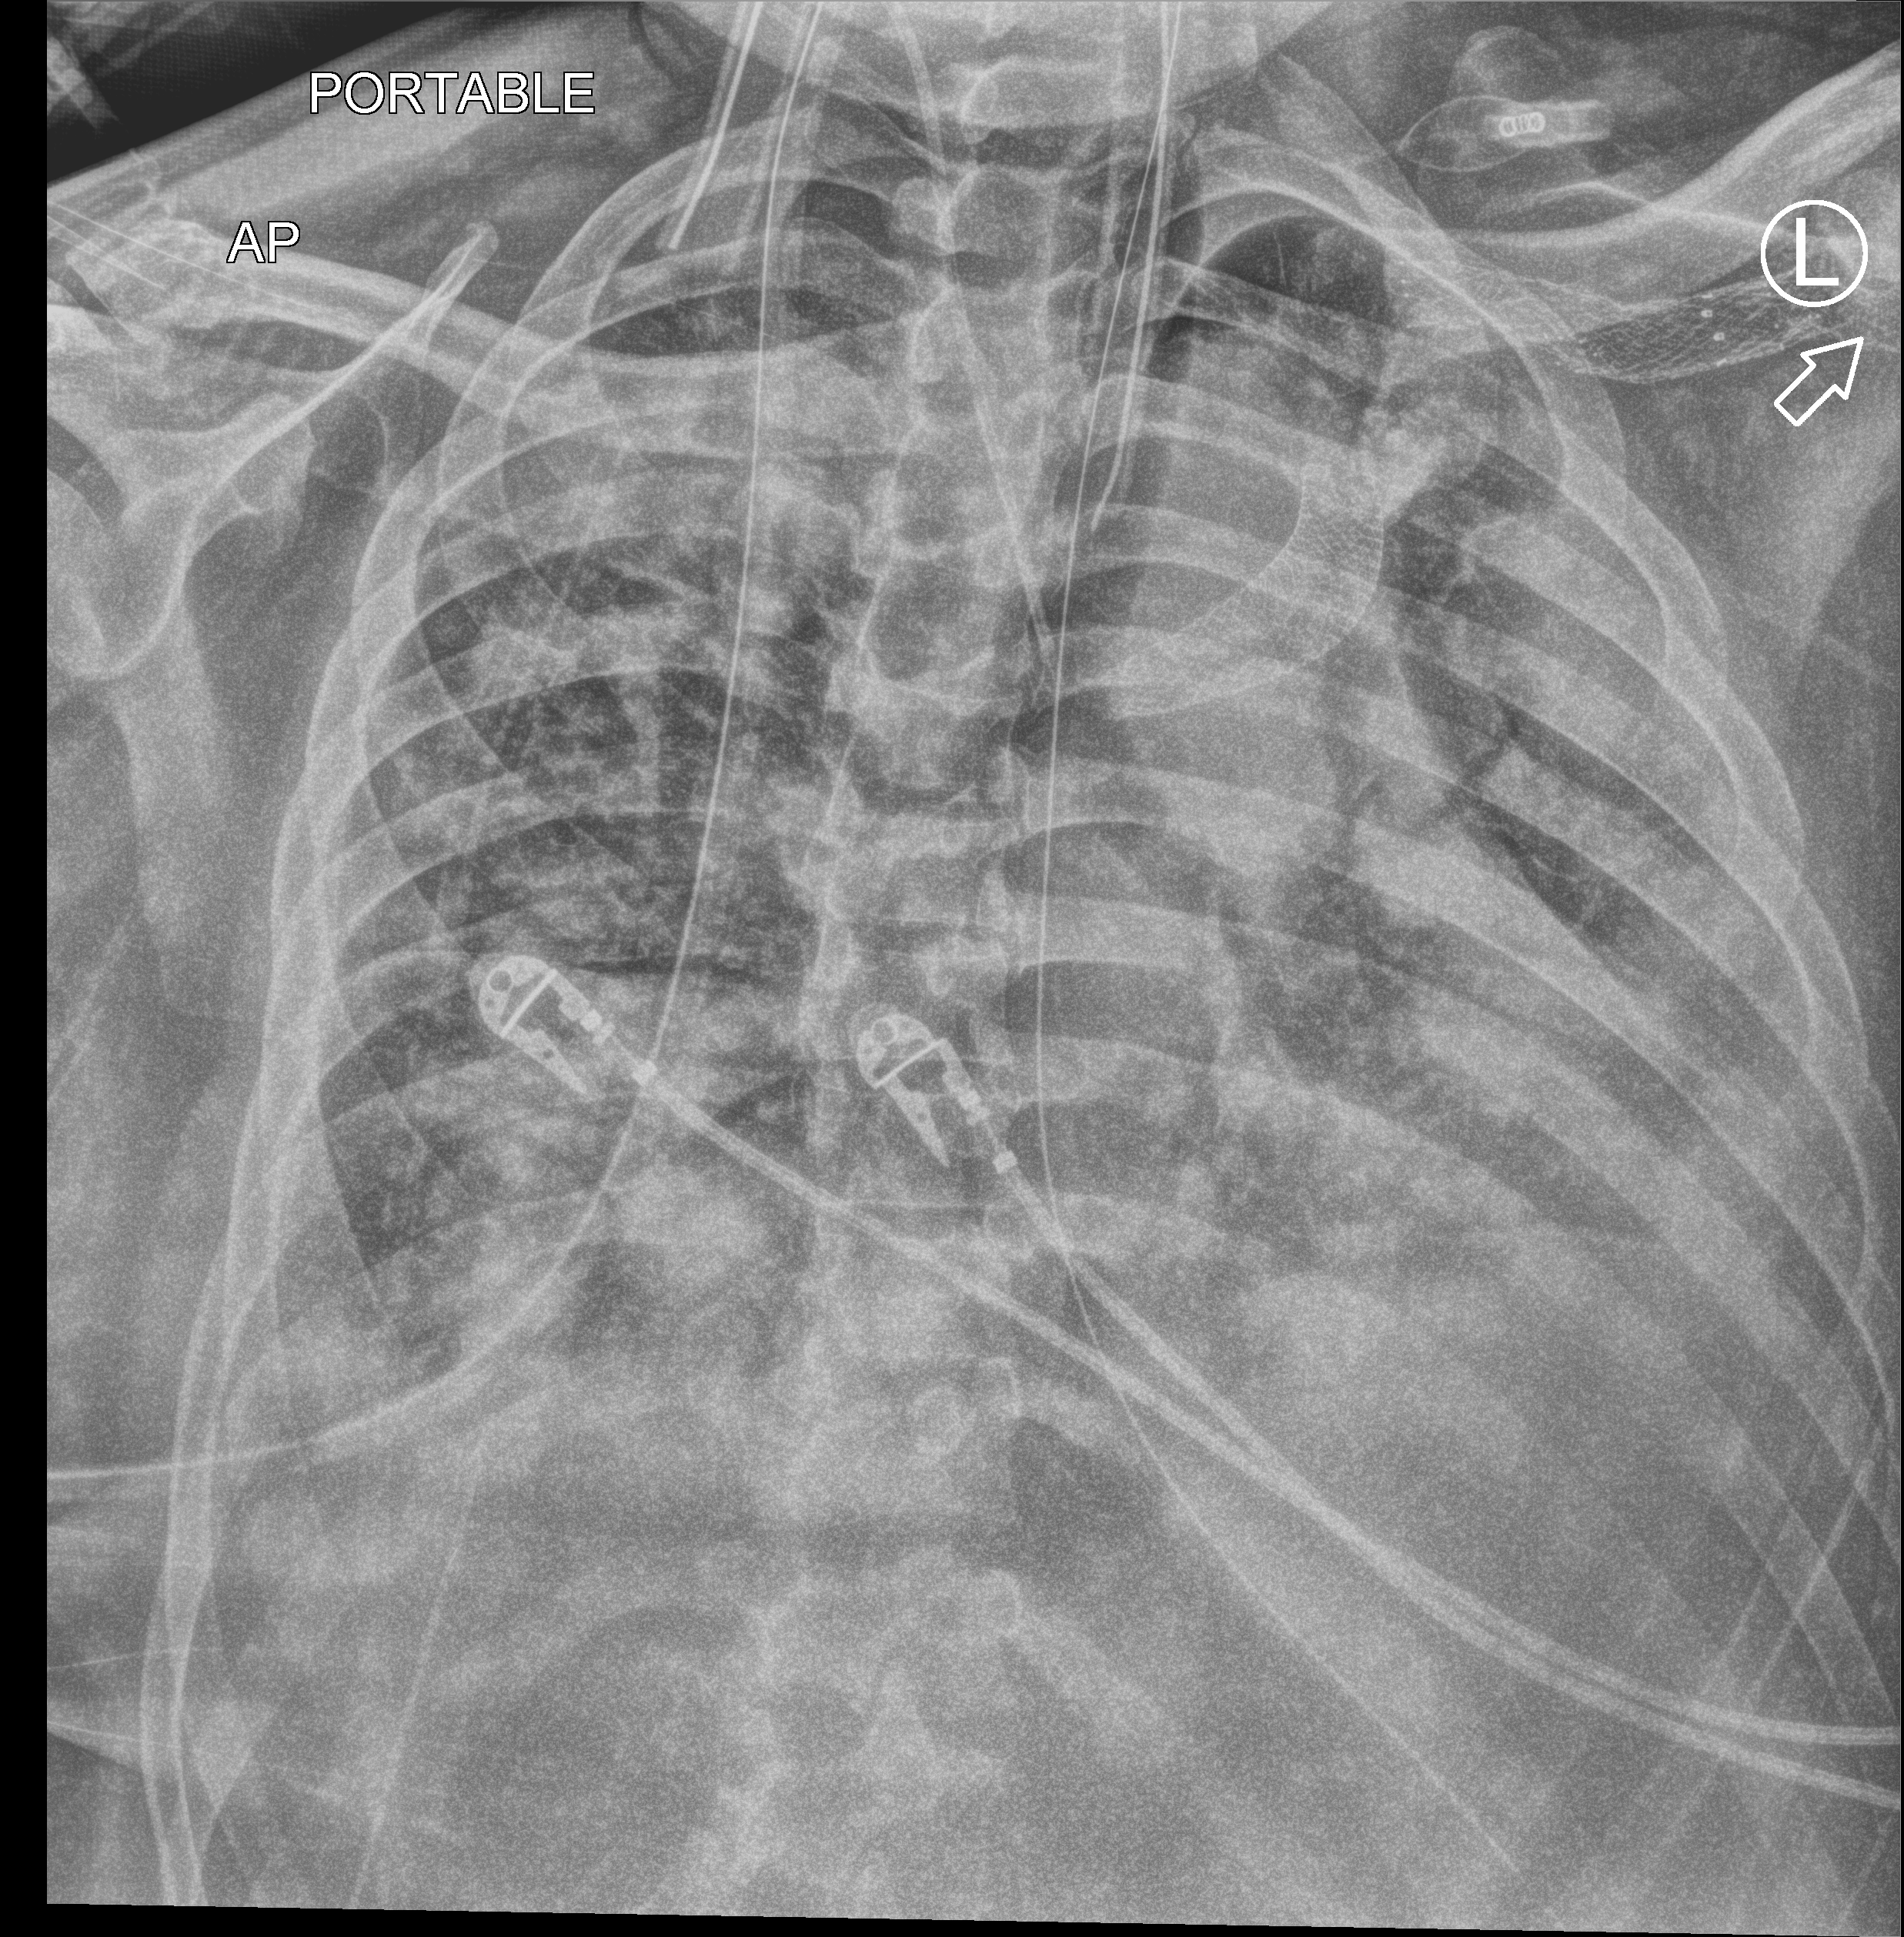
Chest X-ray (portable), anteroposterior (AP) projection. Male patient hospitalised with COVID-19, age 18–59 years.
Hospital-stay facts (about this admission, not read from this image; timing relative to this image not recorded):
- admitted to intensive care during this hospital stay: yes
- mechanically ventilated during this hospital stay: yes
- length of hospital stay: 41 days